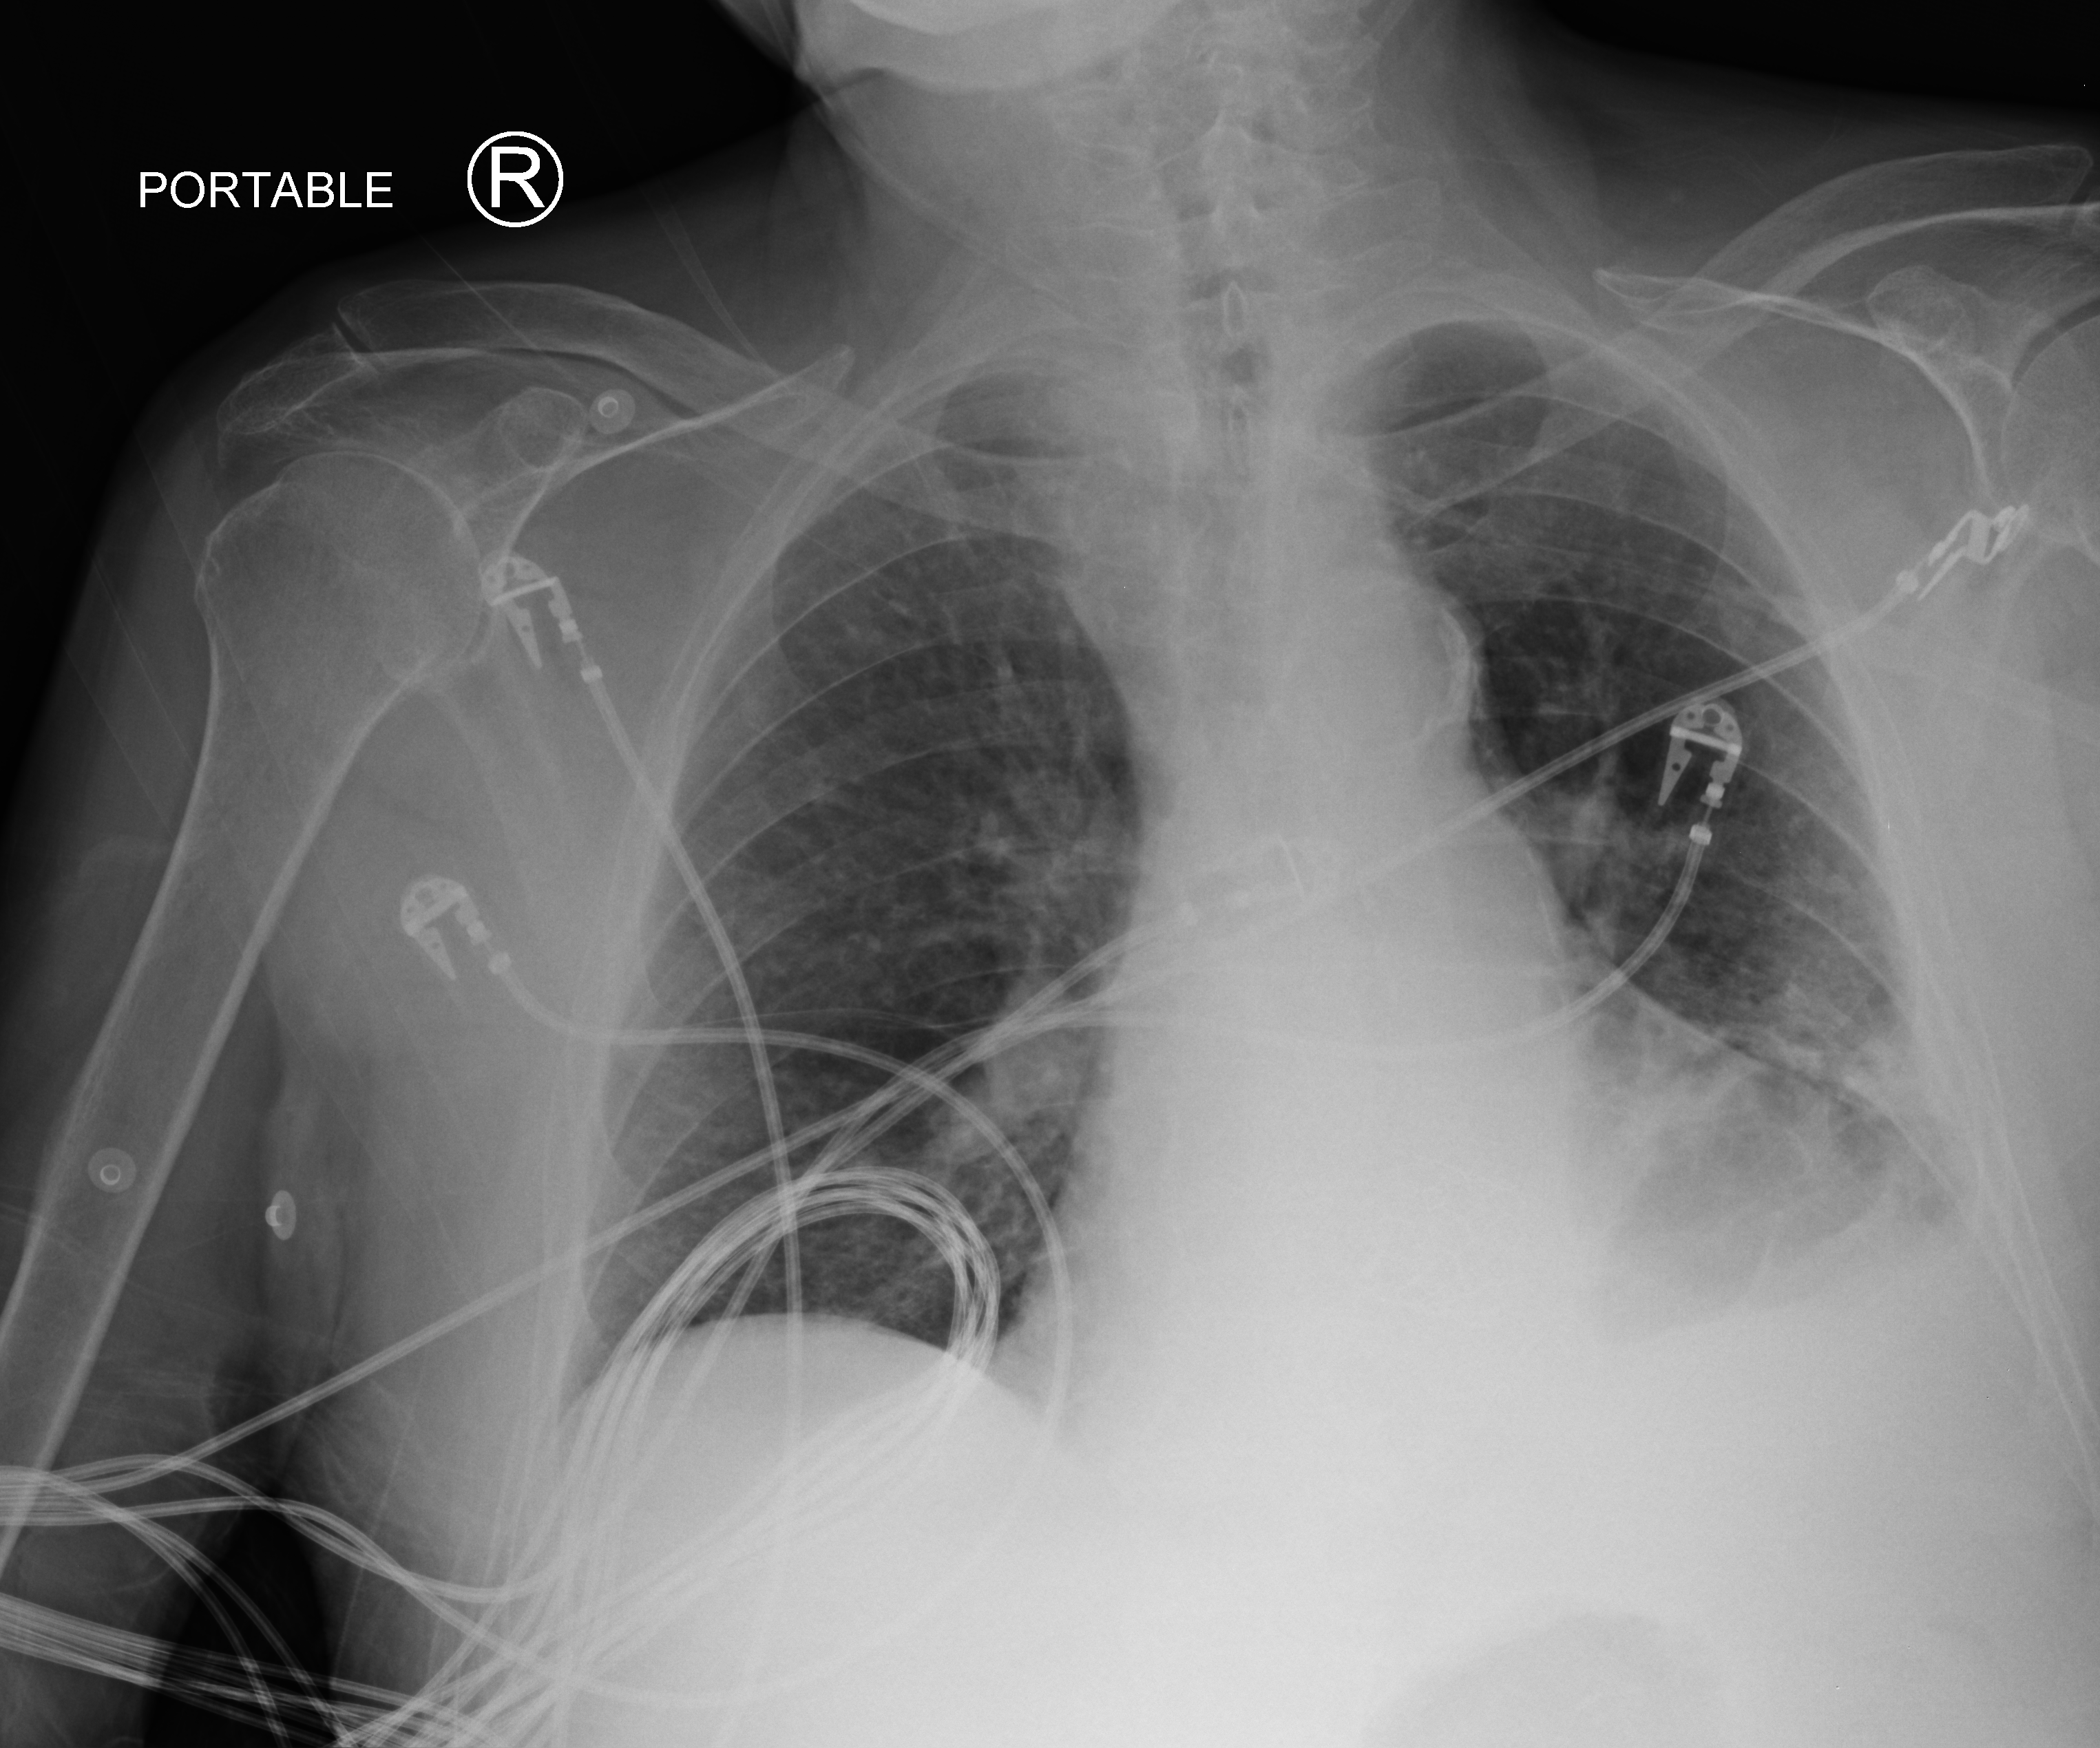
Chest X-ray (portable). Male patient hospitalised with COVID-19, age 75–90 years.
Hospital-stay facts (about this admission, not read from this image; timing relative to this image not recorded): chronic kidney disease (admission record): no; length of hospital stay: 8 days; admitted to intensive care during this hospital stay: yes.